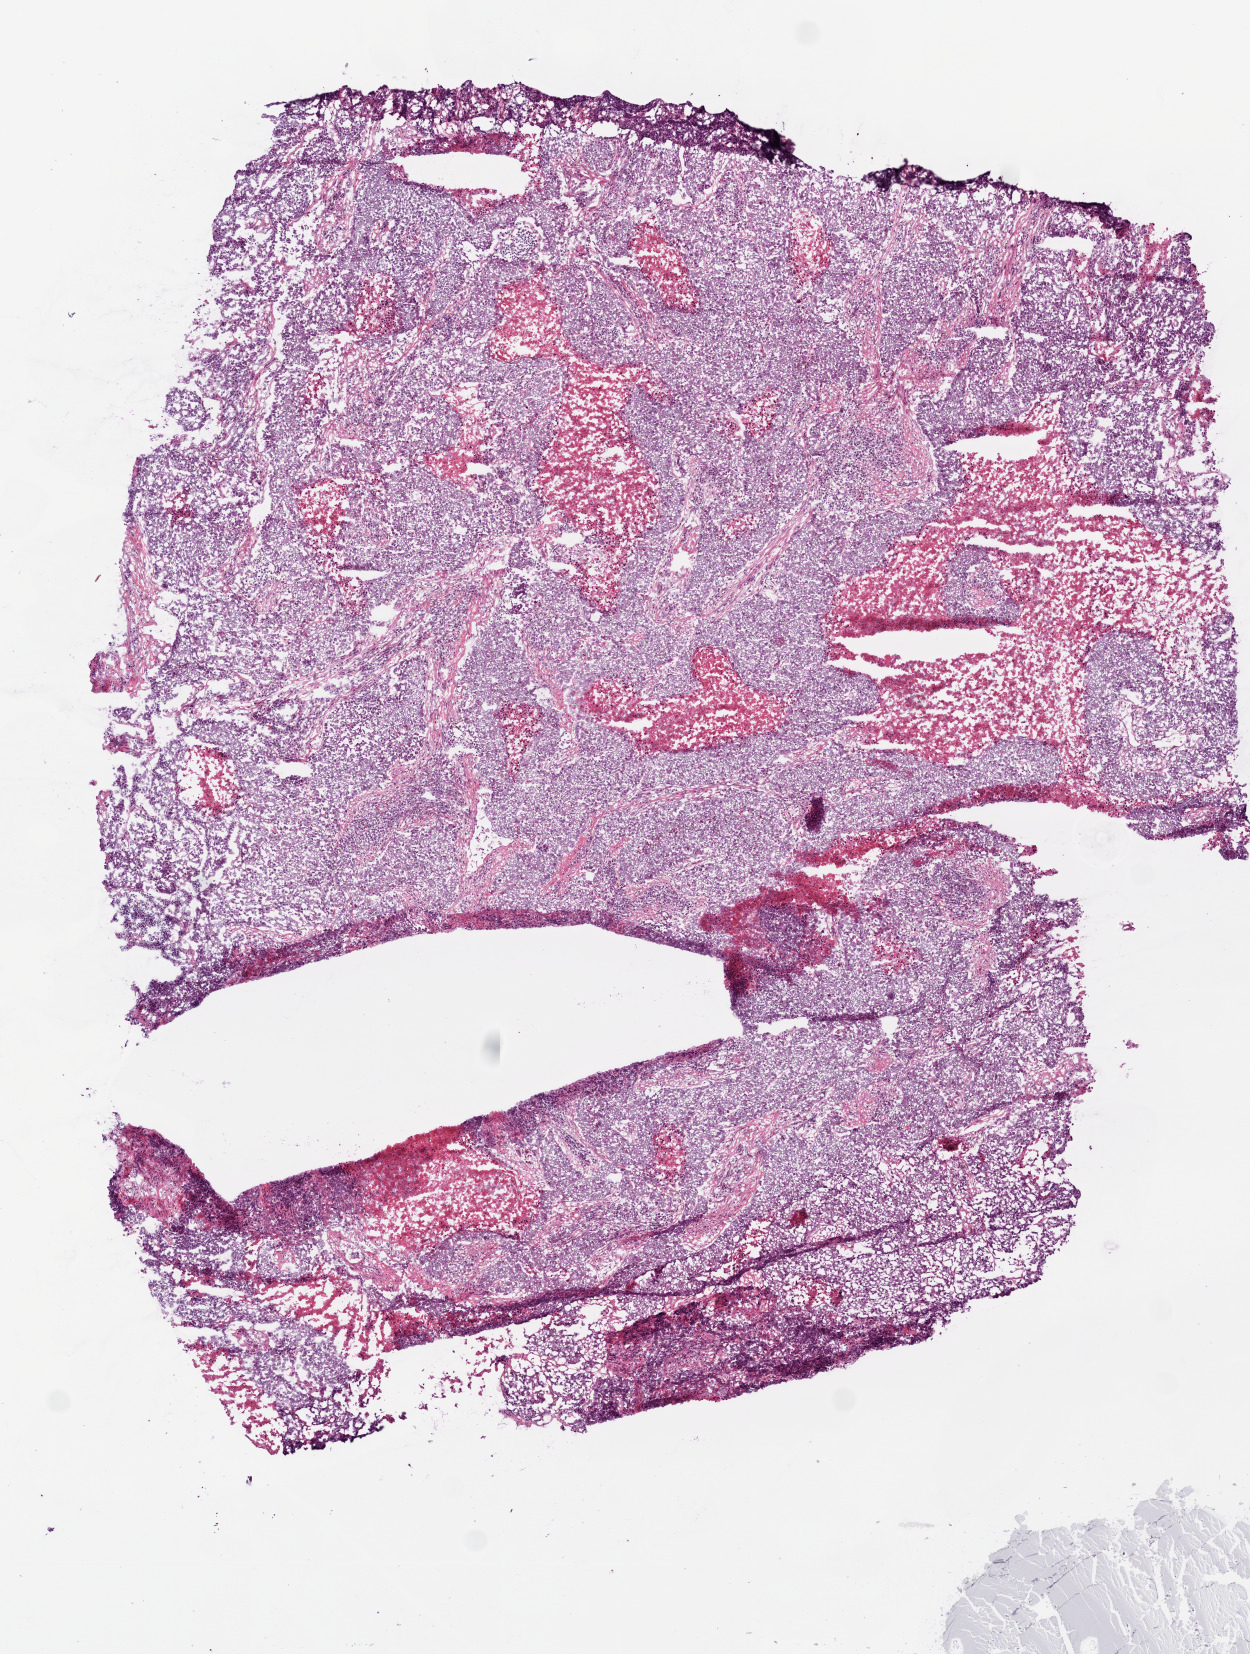
Digitized H&E tissue section (whole slide) — a low-resolution overview of the entire scanned area, about 5.0 x 6.6 mm (from a 20x scan), frozen section from the bottom of the tissue portion, lung, primary tumour sample. Male patient; age at initial diagnosis 63 years. Slide review estimates, as recorded: tumour cells 75%, tumour nuclei 85%, normal cells 0%, stromal cells 10%, necrosis 15%.
AJCC pathologic stage: IIB. Pathologic diagnosis: Squamous cell carcinoma, NOS (lower lobe, lung). Laterality: left.